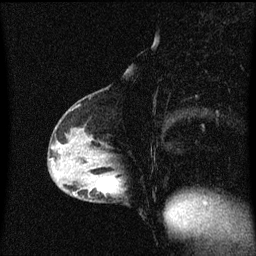
Breast MRI (dynamic contrast-enhanced), one sagittal slice; position 29 of 60 along the scan axis; dynamic contrast-enhanced series, image 2 of 3 at this slice position (ordered by acquisition); 1.5 T; TE 4.2 ms, TR 8.4 ms; 2 mm slice thickness; 256 × 256 image matrix, field of view 200 × 200 mm. Patient: female, 40 years.
Structures marked on this image (semi-automatic segmentation, software-assisted and operator-edited):
- analysis volume of interest (the breast-tissue region the enhancement analysis was run in; not a lesion): bounding box <82,172,126,203> (left, top, right, bottom; pixels)
- tumour enhancement mask (voxels above the 70 % enhancement threshold inside the analysis volume of interest): <108,176,119,193>